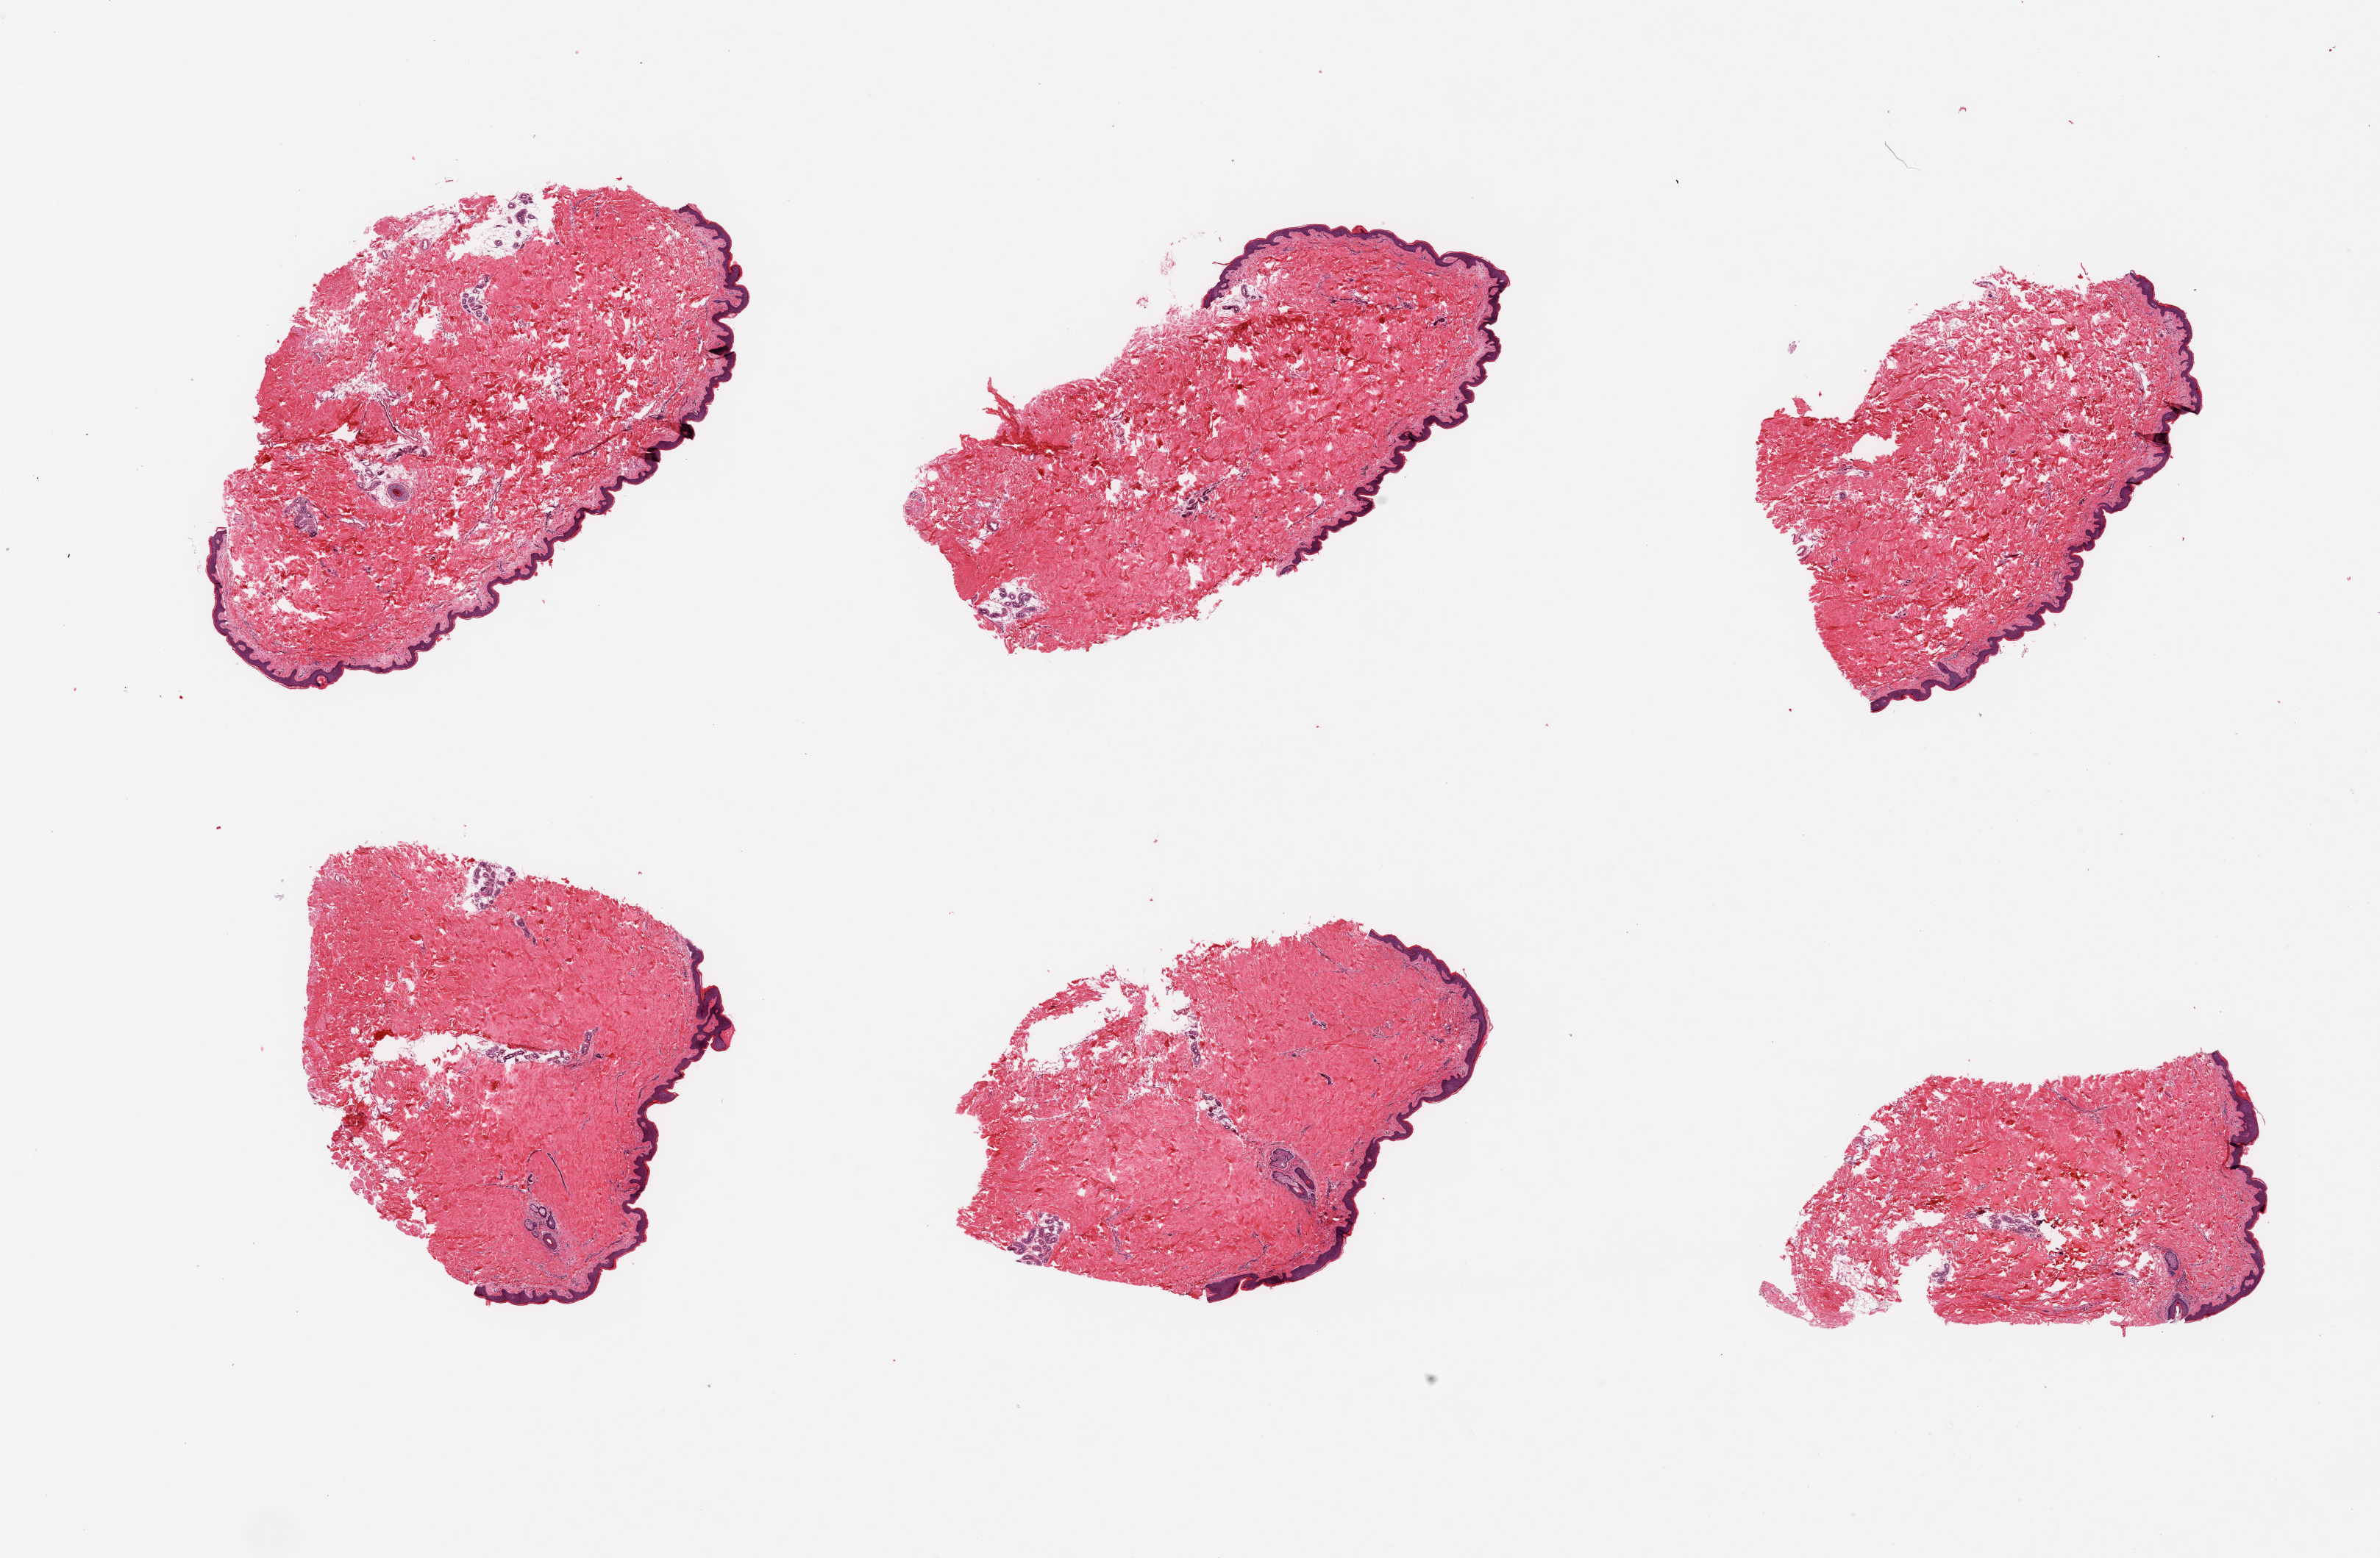
Whole-slide image, H&E stain, whole scanned area (about 25.6 x 16.8 mm, acquisition: 20x scan) shown as a low-resolution overview. PAXgene-fixed, paraffin-embedded tissue. Target tissue: skin of suprapubic region. Donor tissue sample. Donor sex: male.
Reviewer comment on this tissue sample: 6 pieces, well trimmed with trivial amount of fat.